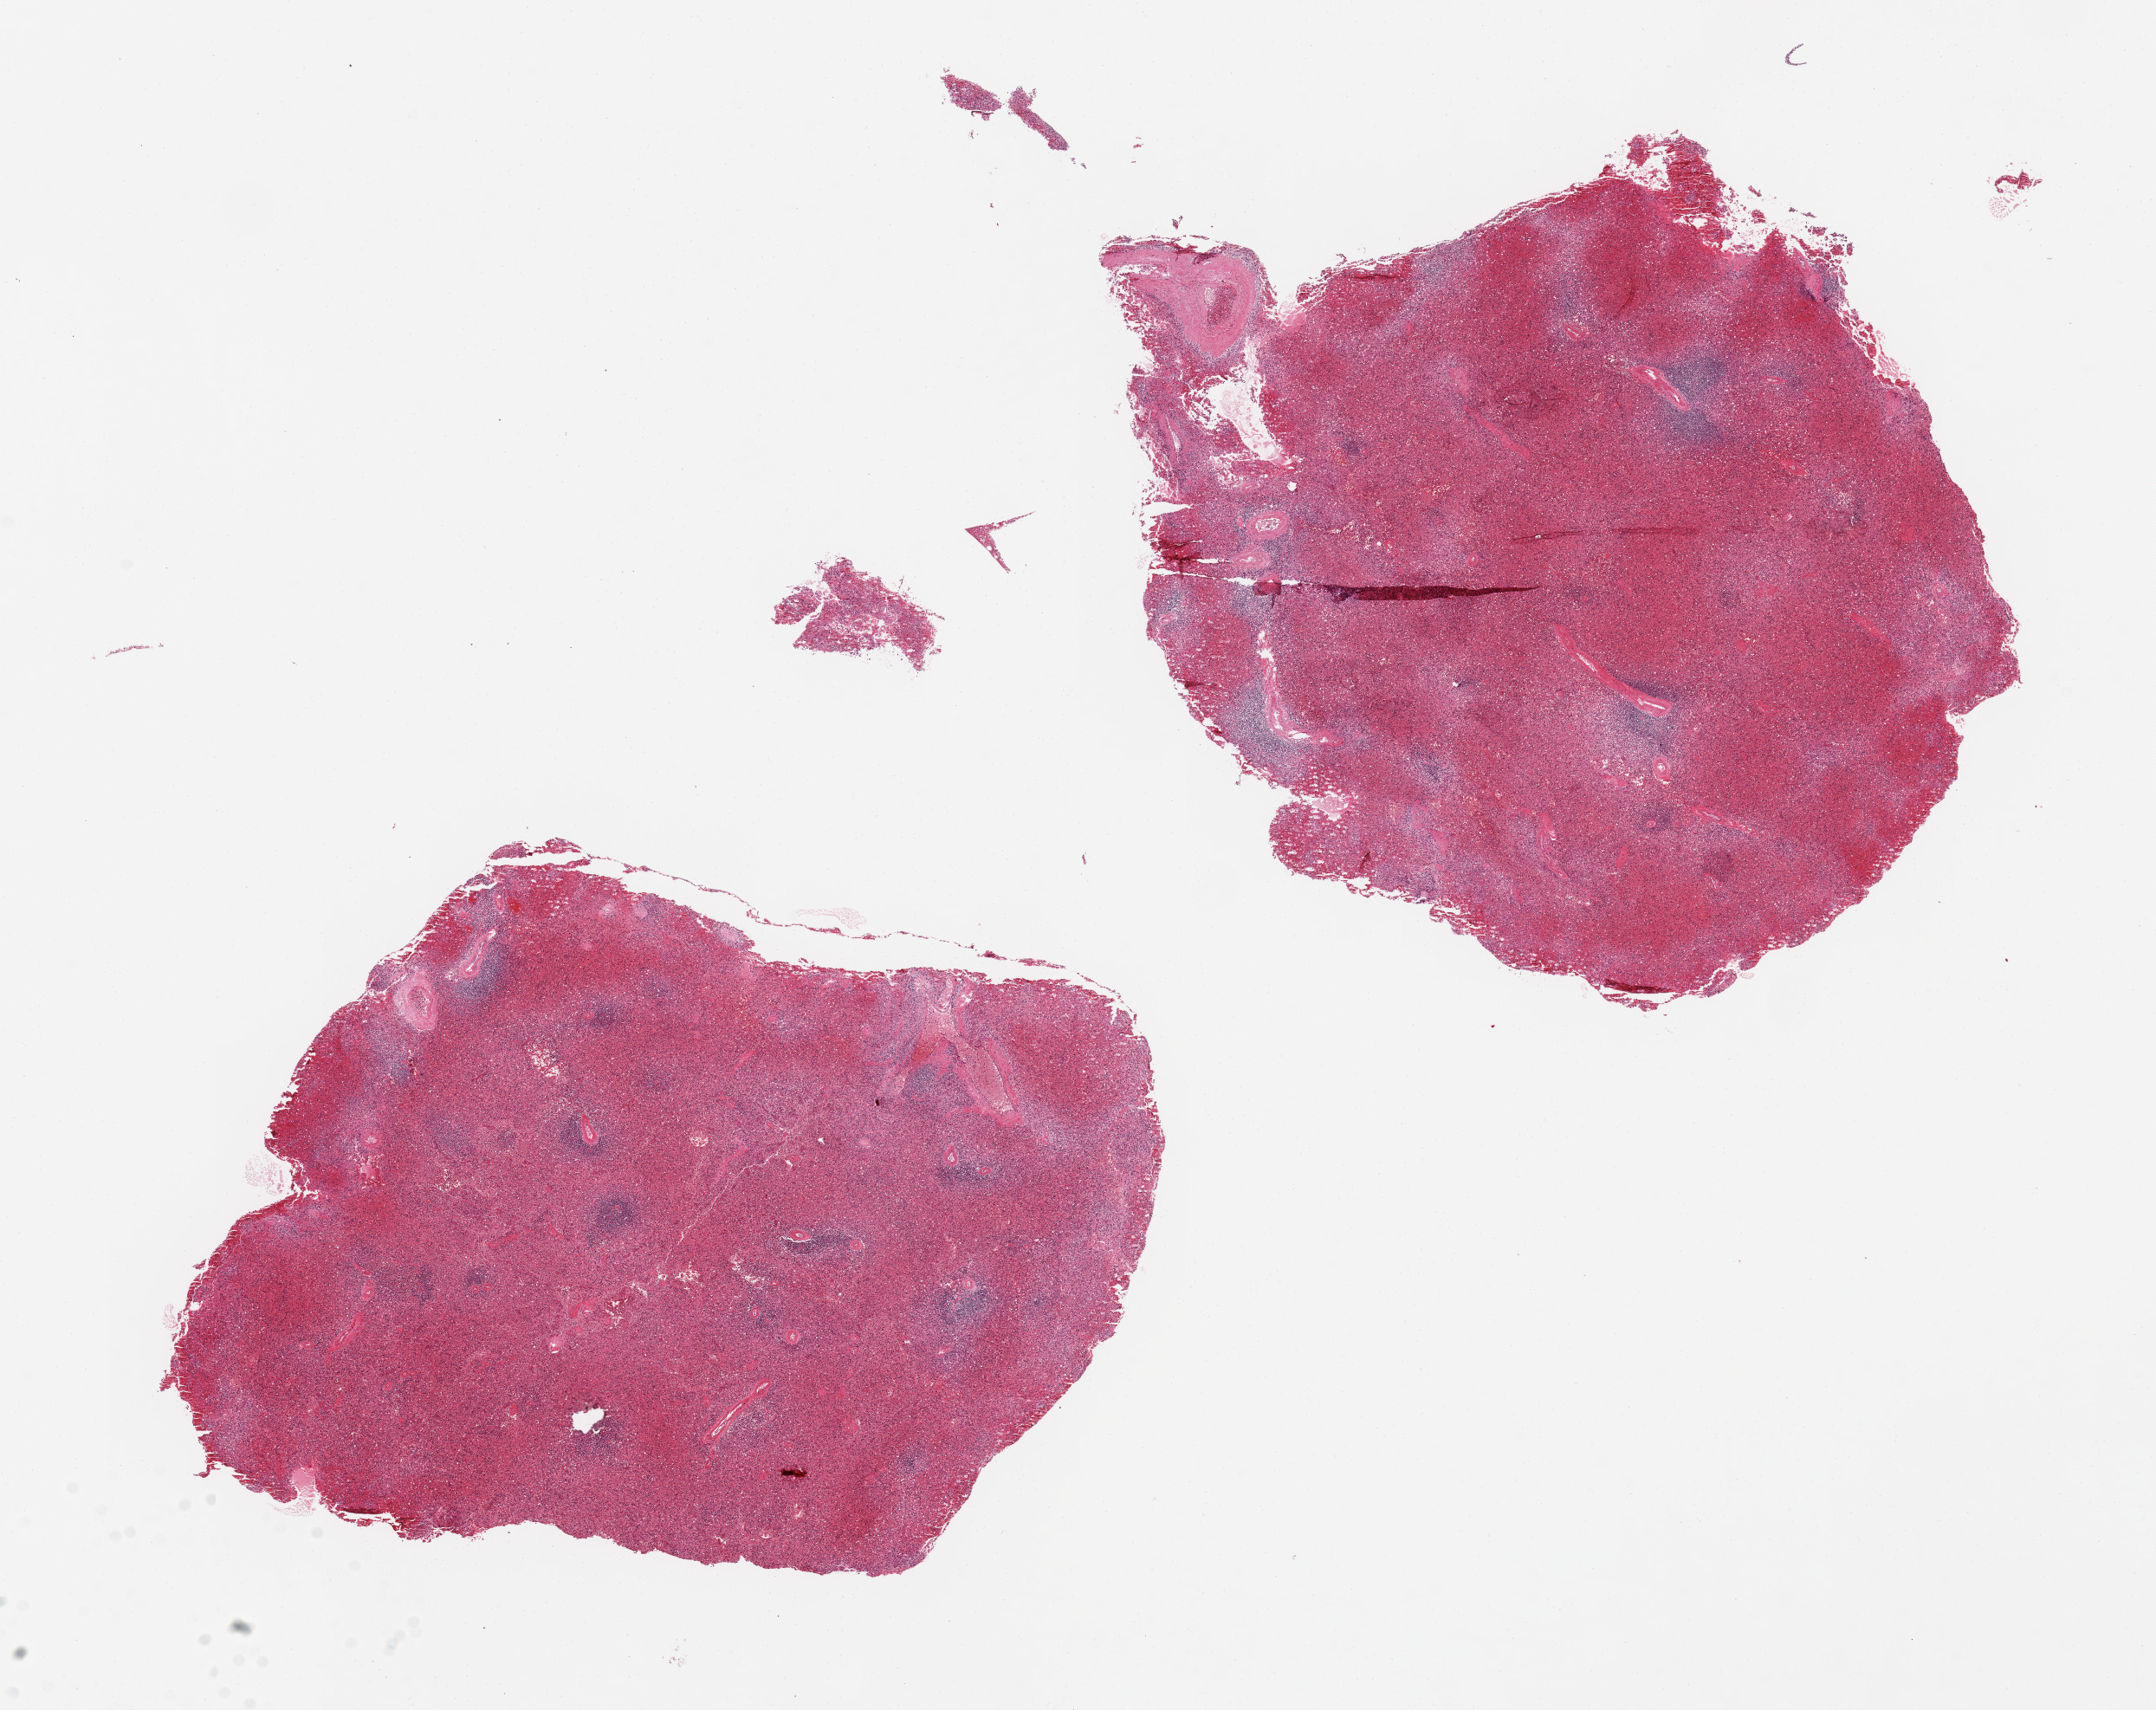
Haematoxylin and eosin whole-slide image, brightfield — shown as a low-resolution overview of the whole scanned area (about 19.7 x 15.6 mm, slide scanned at 20x). PAXgene-fixed, paraffin-embedded tissue. Sampled site (target tissue): spleen. Donor tissue sample. Donor: male.
Reviewer comment on this tissue sample: 2 pieces. 8x6.5 & 9x8mm.